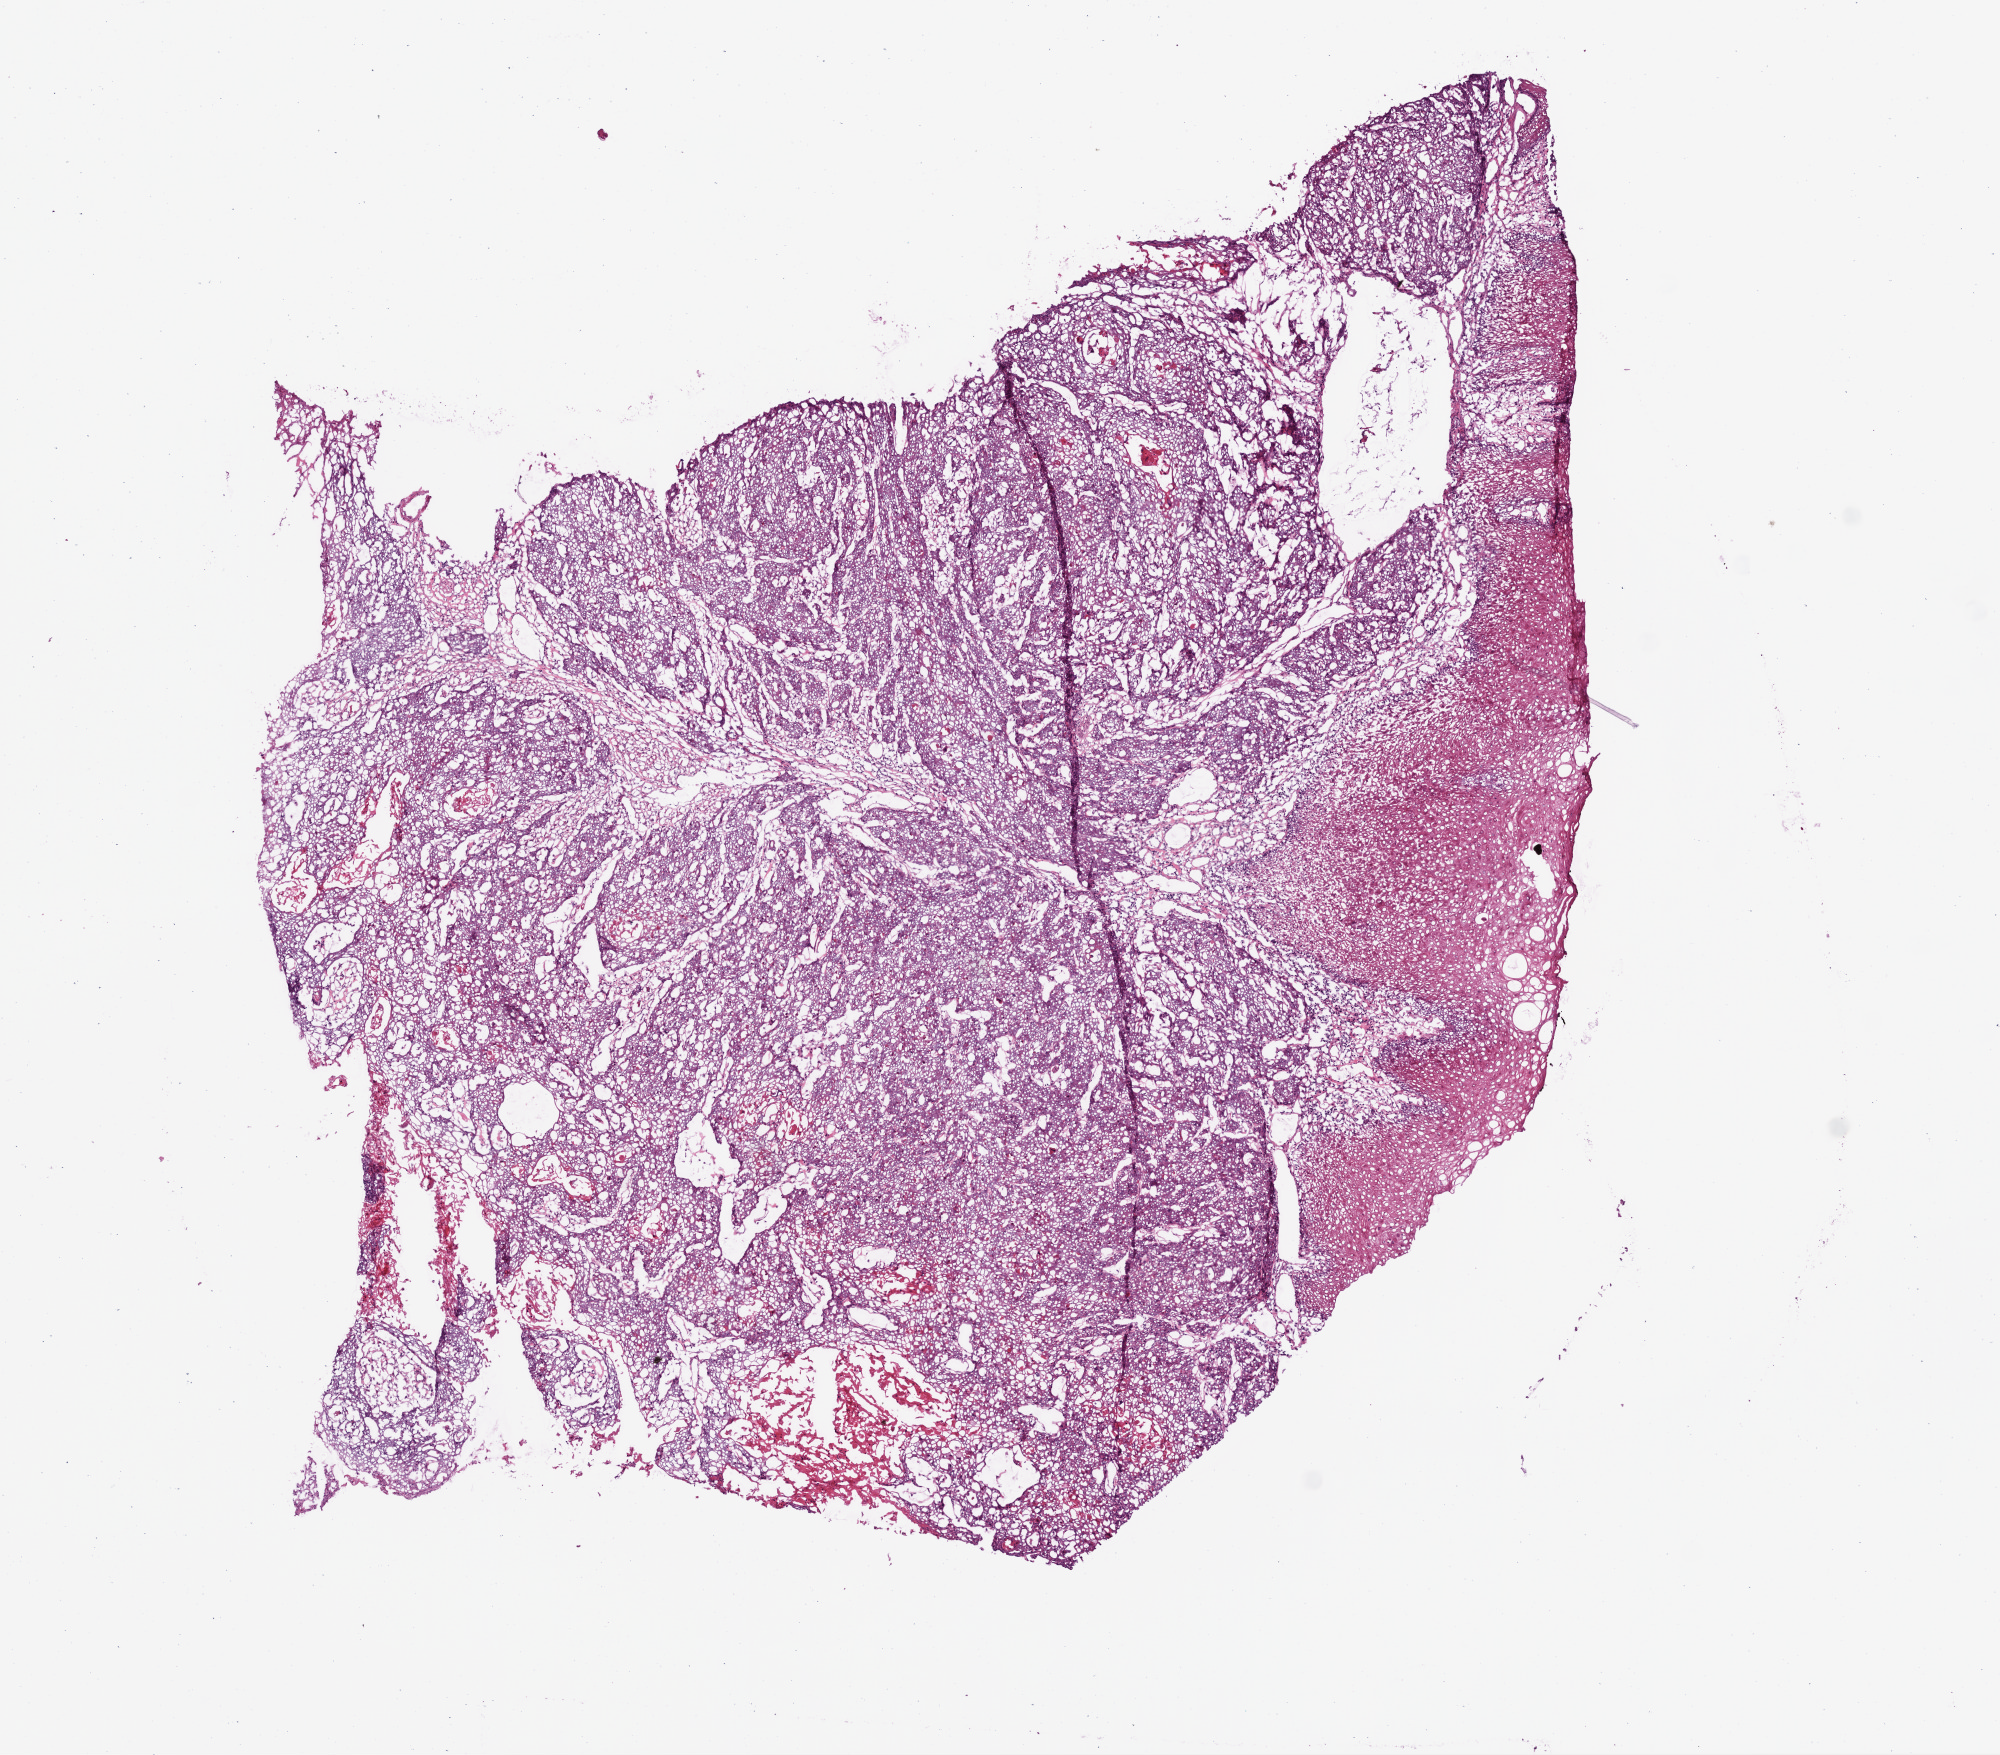
Whole-slide histology image, H&E-stained — a low-resolution overview of the entire scanned area, about 8.0 x 7.0 mm (slide scanned at 20x). Frozen section from the bottom of the tissue portion. Head and neck, primary tumour sample. Male, age 52 years at initial diagnosis. Histologic grade: G2 (moderately differentiated). Pathologist review of this section (percent, as recorded): tumour cells 80%, tumour nuclei 70%, normal cells 18%, necrosis 2%. Inflammatory infiltration, as recorded: lymphocyte infiltration 20%.
Laterality: left. Histologic diagnosis: Squamous cell carcinoma, NOS (tongue, NOS). AJCC pathologic stage: IVA (7th edition).